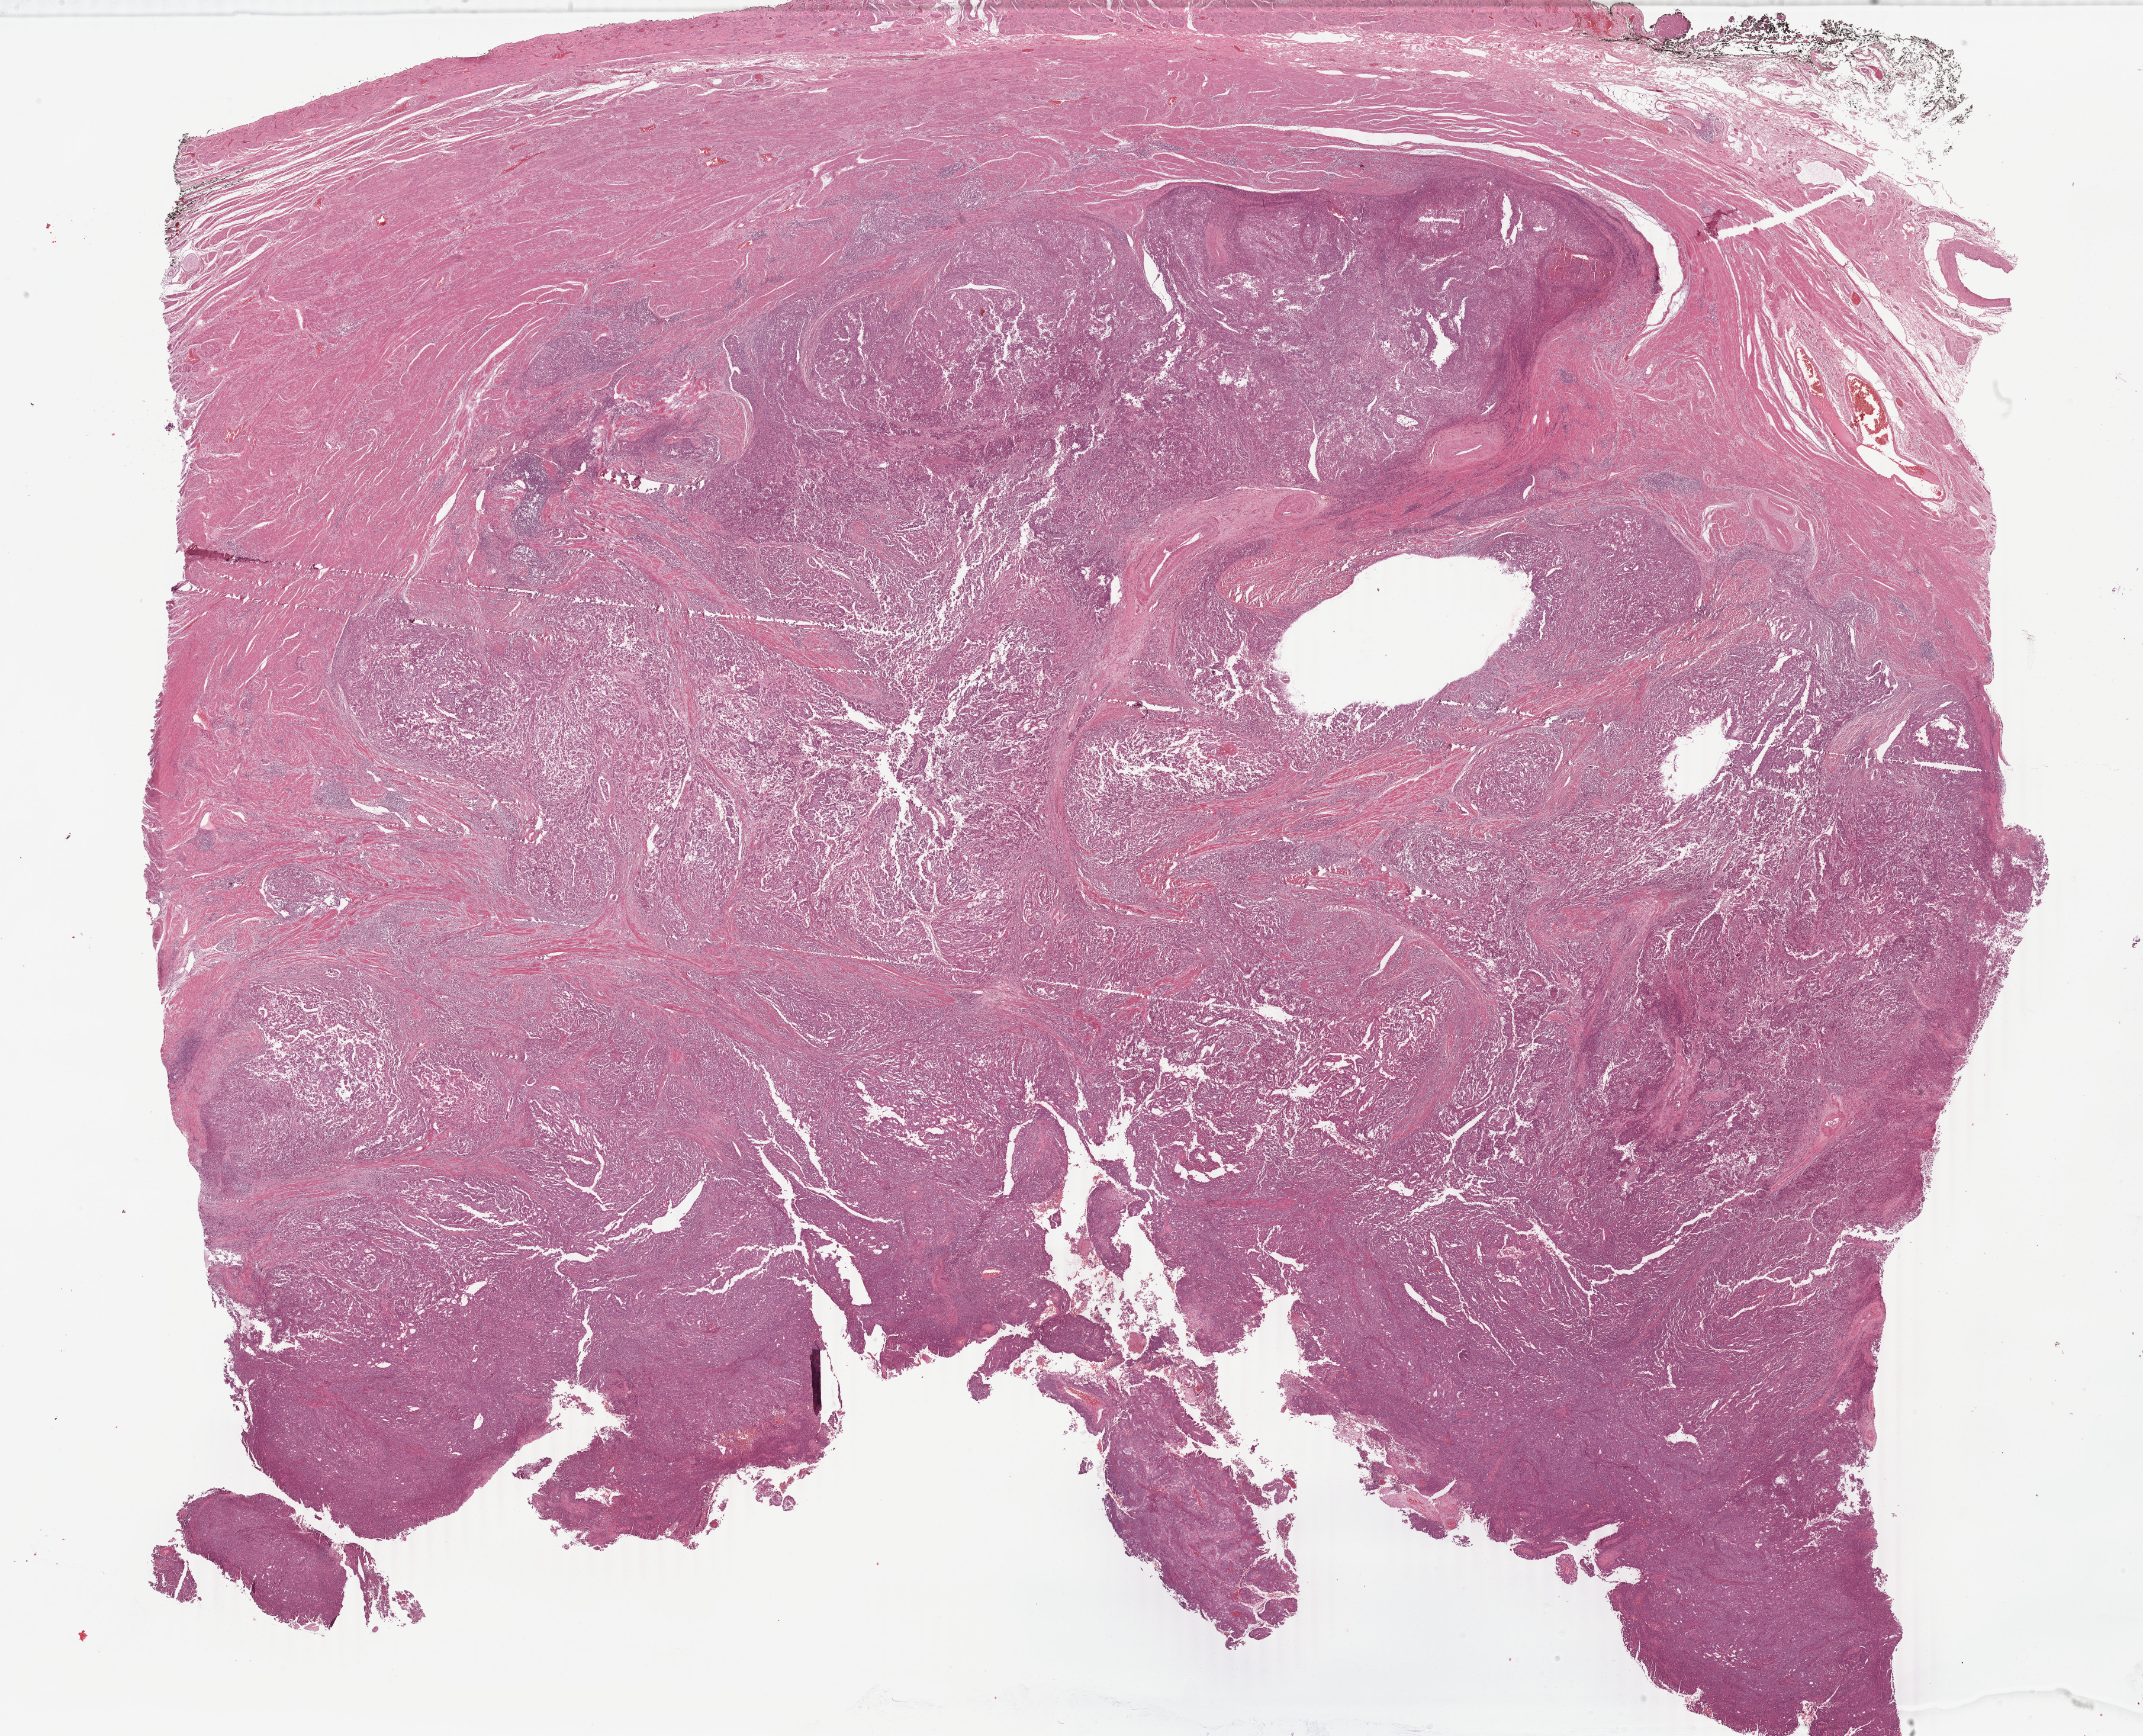
Digitized H&E-stained tissue section (whole slide) — low-resolution overview of the scanned area, about 28.8 x 23.3 mm (acquisition: 40x scan); formalin-fixed paraffin-embedded (FFPE) diagnostic section; sample: primary tumour, uterus. Patient: female, age at initial diagnosis 58 years. Histologic grade: G3 (poorly differentiated).
Diagnosis: Endometrioid adenocarcinoma, NOS (endometrium). FIGO stage: IVB. Lymph nodes positive (case pathology): 2 of 14 examined.